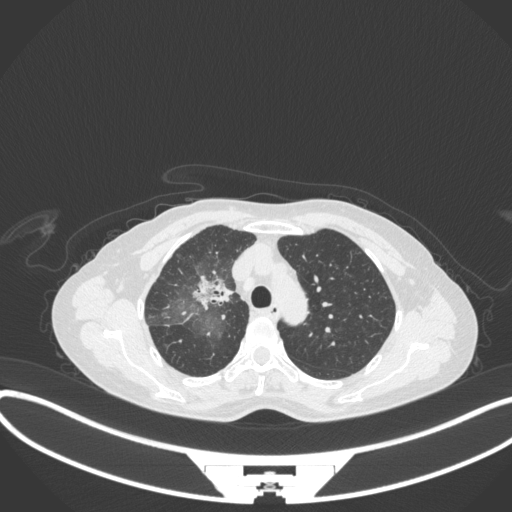
Chest CT, one axial slice. Slice 236 of 311 in the series (ordered by position). Reconstruction kernel B31f. 120 kVp. Lung window (W 1500 / L -600 HU). 1 mm slice thickness. 512 × 512 image matrix. Female patient, age 59 years. Case-level facts recorded for this patient, not image findings: clinical TNM (as recorded): T3 N0 M0.
Outlined on this slice (rectangle marked by the reading radiologist):
- lung tumour (recorded histology: adenocarcinoma): box from (x=185, y=265) to (x=234, y=314) px